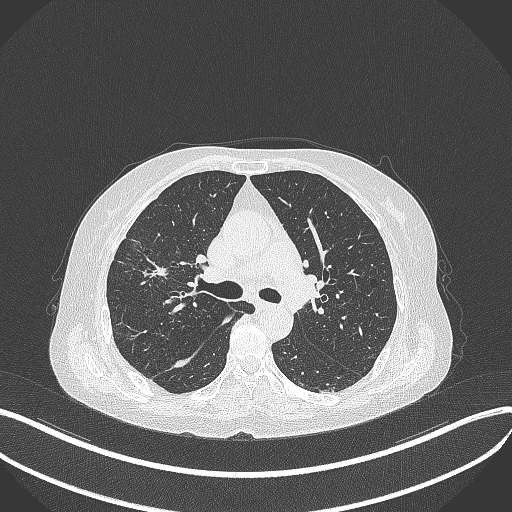
Chest CT, one axial slice; slice 255 of 429 in the series (ordered by position); reconstruction kernel B70f; 120 kVp; lung window (W 1500 / L -600 HU); 1 mm slice thickness; 512 × 512 image matrix. Female patient, age 69 years. From the clinical record (not read from this slice): clinical TNM (as recorded): T1b N3 M0.
Structures marked on this image (bounding box drawn by a radiologist):
- lung tumour (recorded histology: small cell carcinoma): bounding box <137,253,177,286> (left, top, right, bottom; pixels)